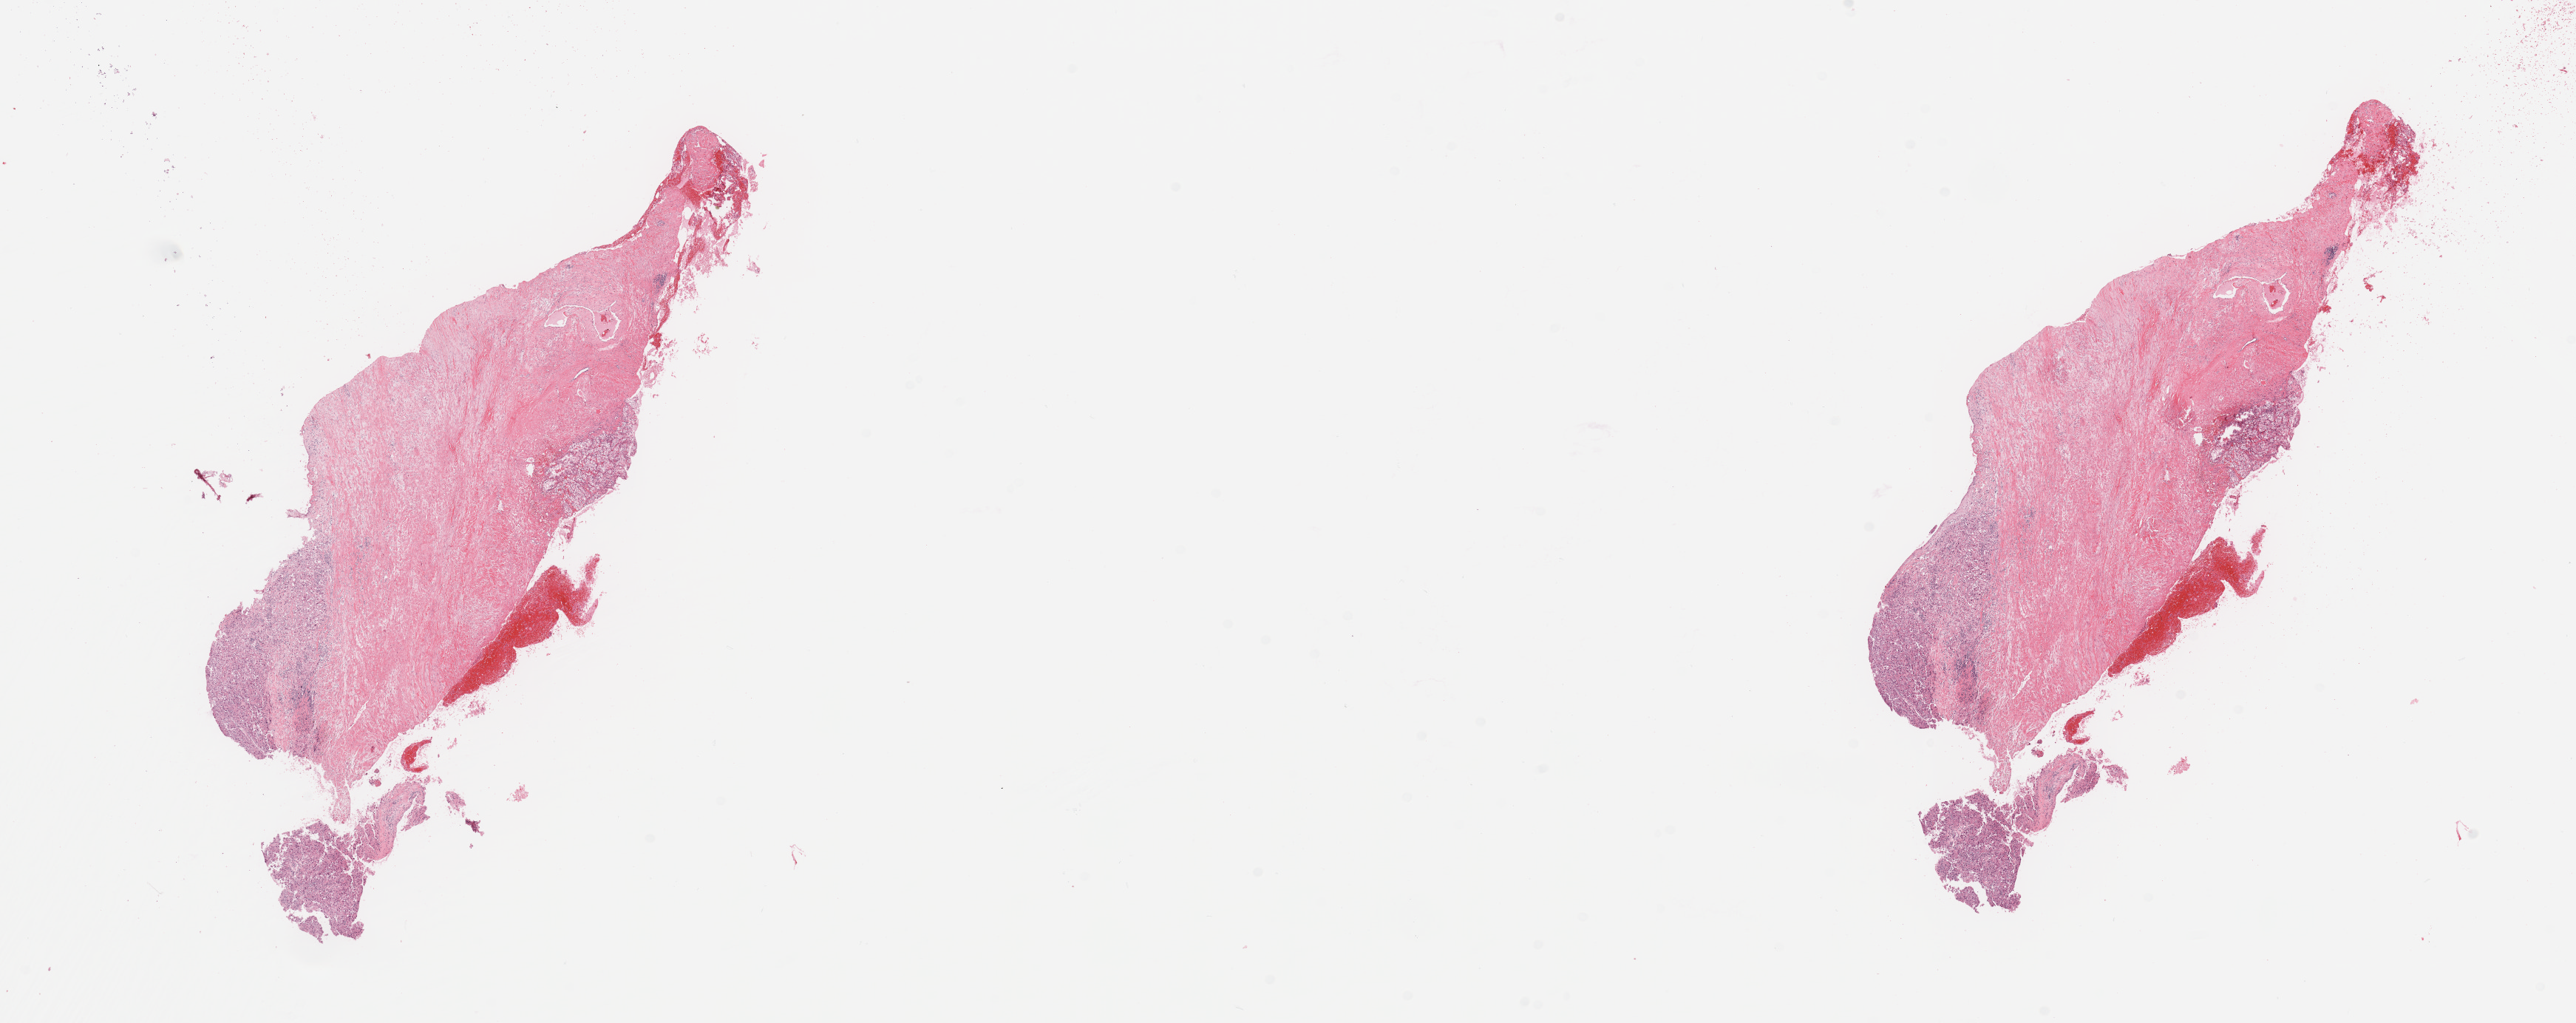
H&E-stained whole-slide image, shown as a low-resolution overview of the whole scanned area (about 27.6 x 10.9 mm, from a 20x scan); kidney, tumour tissue. Patient: male, age 74 years. Histologic grade: G3 (poorly differentiated).
Diagnosis: Renal cell carcinoma, NOS. AJCC pathologic stage: I. Primary tumour site (as recorded): lower pole.